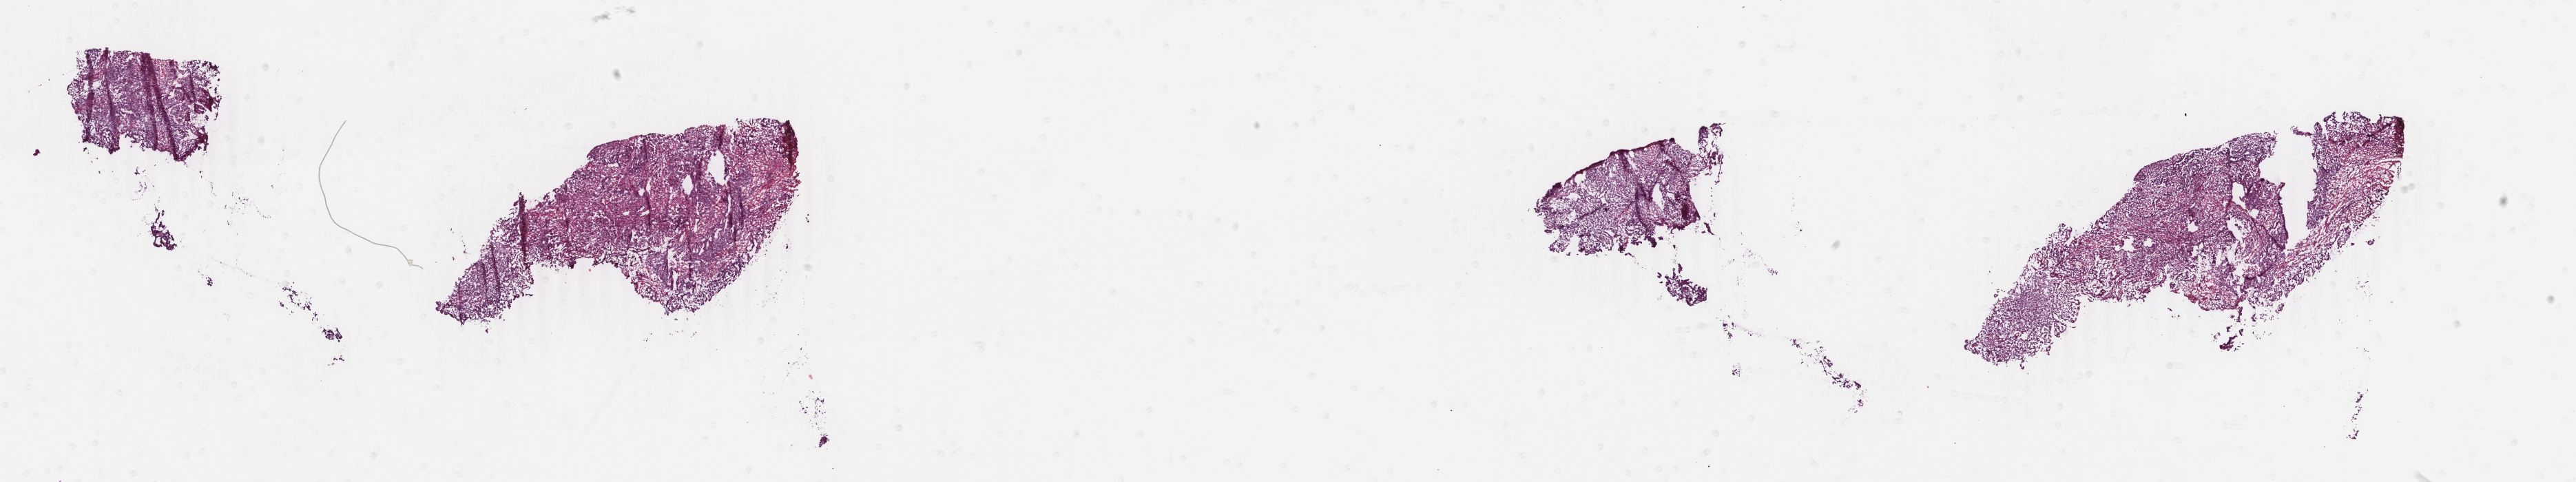
Hematoxylin and eosin (H&E) stained whole-slide image — a low-resolution overview of the entire scanned area, about 29.7 x 5.6 mm; frozen section; sample: primary tumour, uterus. Female, age 53 years at initial diagnosis. Composition of this section per pathologist review: tumour cells 57%, tumour nuclei 55%.
Pathologic diagnosis: Endometrioid adenocarcinoma, NOS.